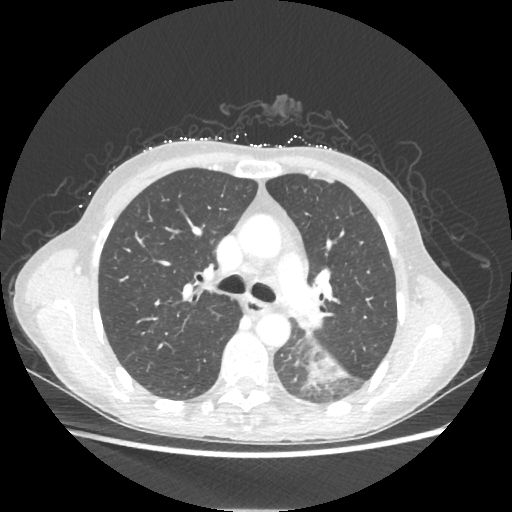
Chest CT, one axial slice; slice 137 of 221 in the series (ordered by position); 80 kVp; lung window (W 1500 / L -600 HU); 1.25 mm slice thickness; 512 × 512 image matrix, field of view 360 × 360 mm. Patient: female, 53 years. From the clinical record (not read from this slice): clinical TNM (as recorded): T3 N0 M0.
Outlined on this slice (bounding box drawn by a radiologist):
- lung tumour (recorded histology: adenocarcinoma): box from (x=307, y=346) to (x=349, y=388) px